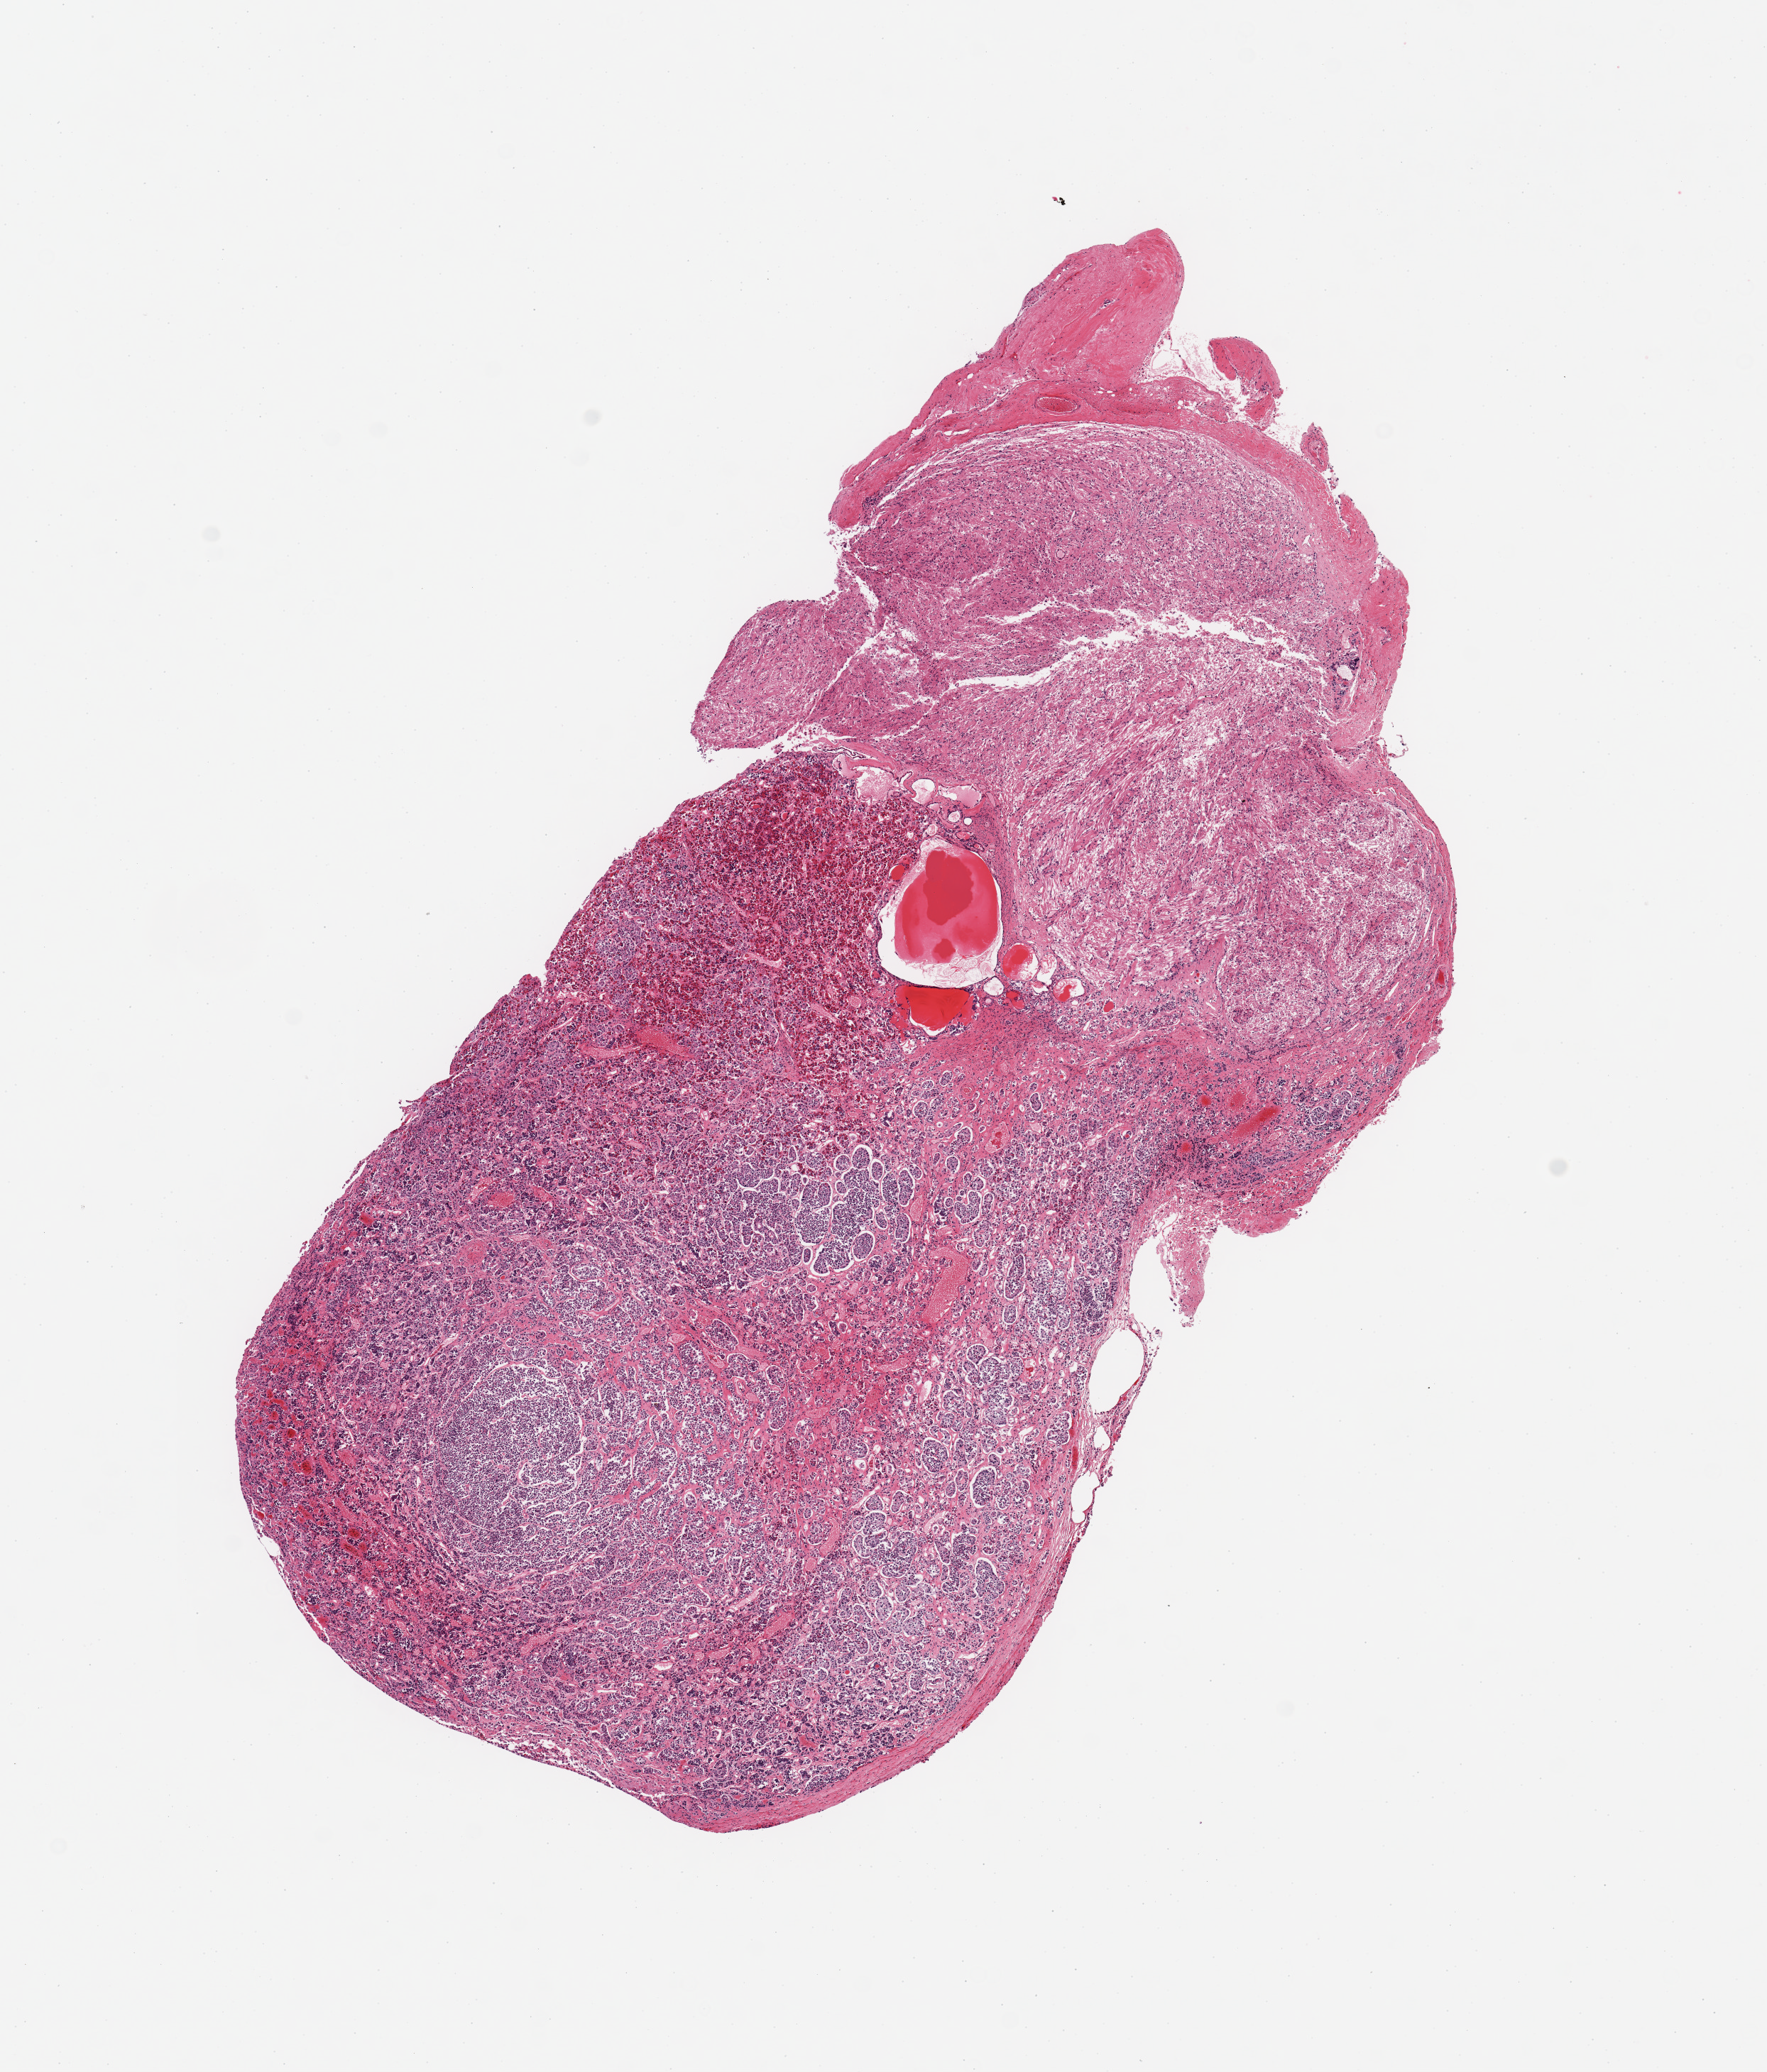
Digitized hematoxylin and eosin (H&E)-stained section, low-resolution overview of the scanned area, about 9.8 x 11.5 mm; PAXgene-fixed paraffin-embedded (PFPE) section; sampled site (target tissue): pituitary; tissue donor sample. Female donor.
Review note (as recorded): 1 piece; adeno:neurohypophysis= 60:40%.